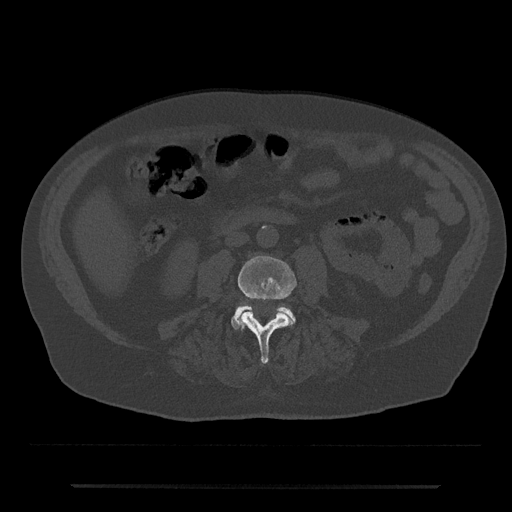
CT including the spine, one axial slice; position 391 of 797 along the scan axis; bone window (W 1800 / L 400 HU); 0.5 mm slice thickness; 512 × 512 image matrix, field of view 434 × 434 mm. Male patient, age 80 years. From the clinical record (not read from this slice): primary cancer: prostate.
Annotated regions visible in this slice (semi-automatically segmented with operator editing):
- L3 vertebra: bounding box <237,256,297,364> (left, top, right, bottom; pixels)
- L4 vertebra: <231,305,296,329>